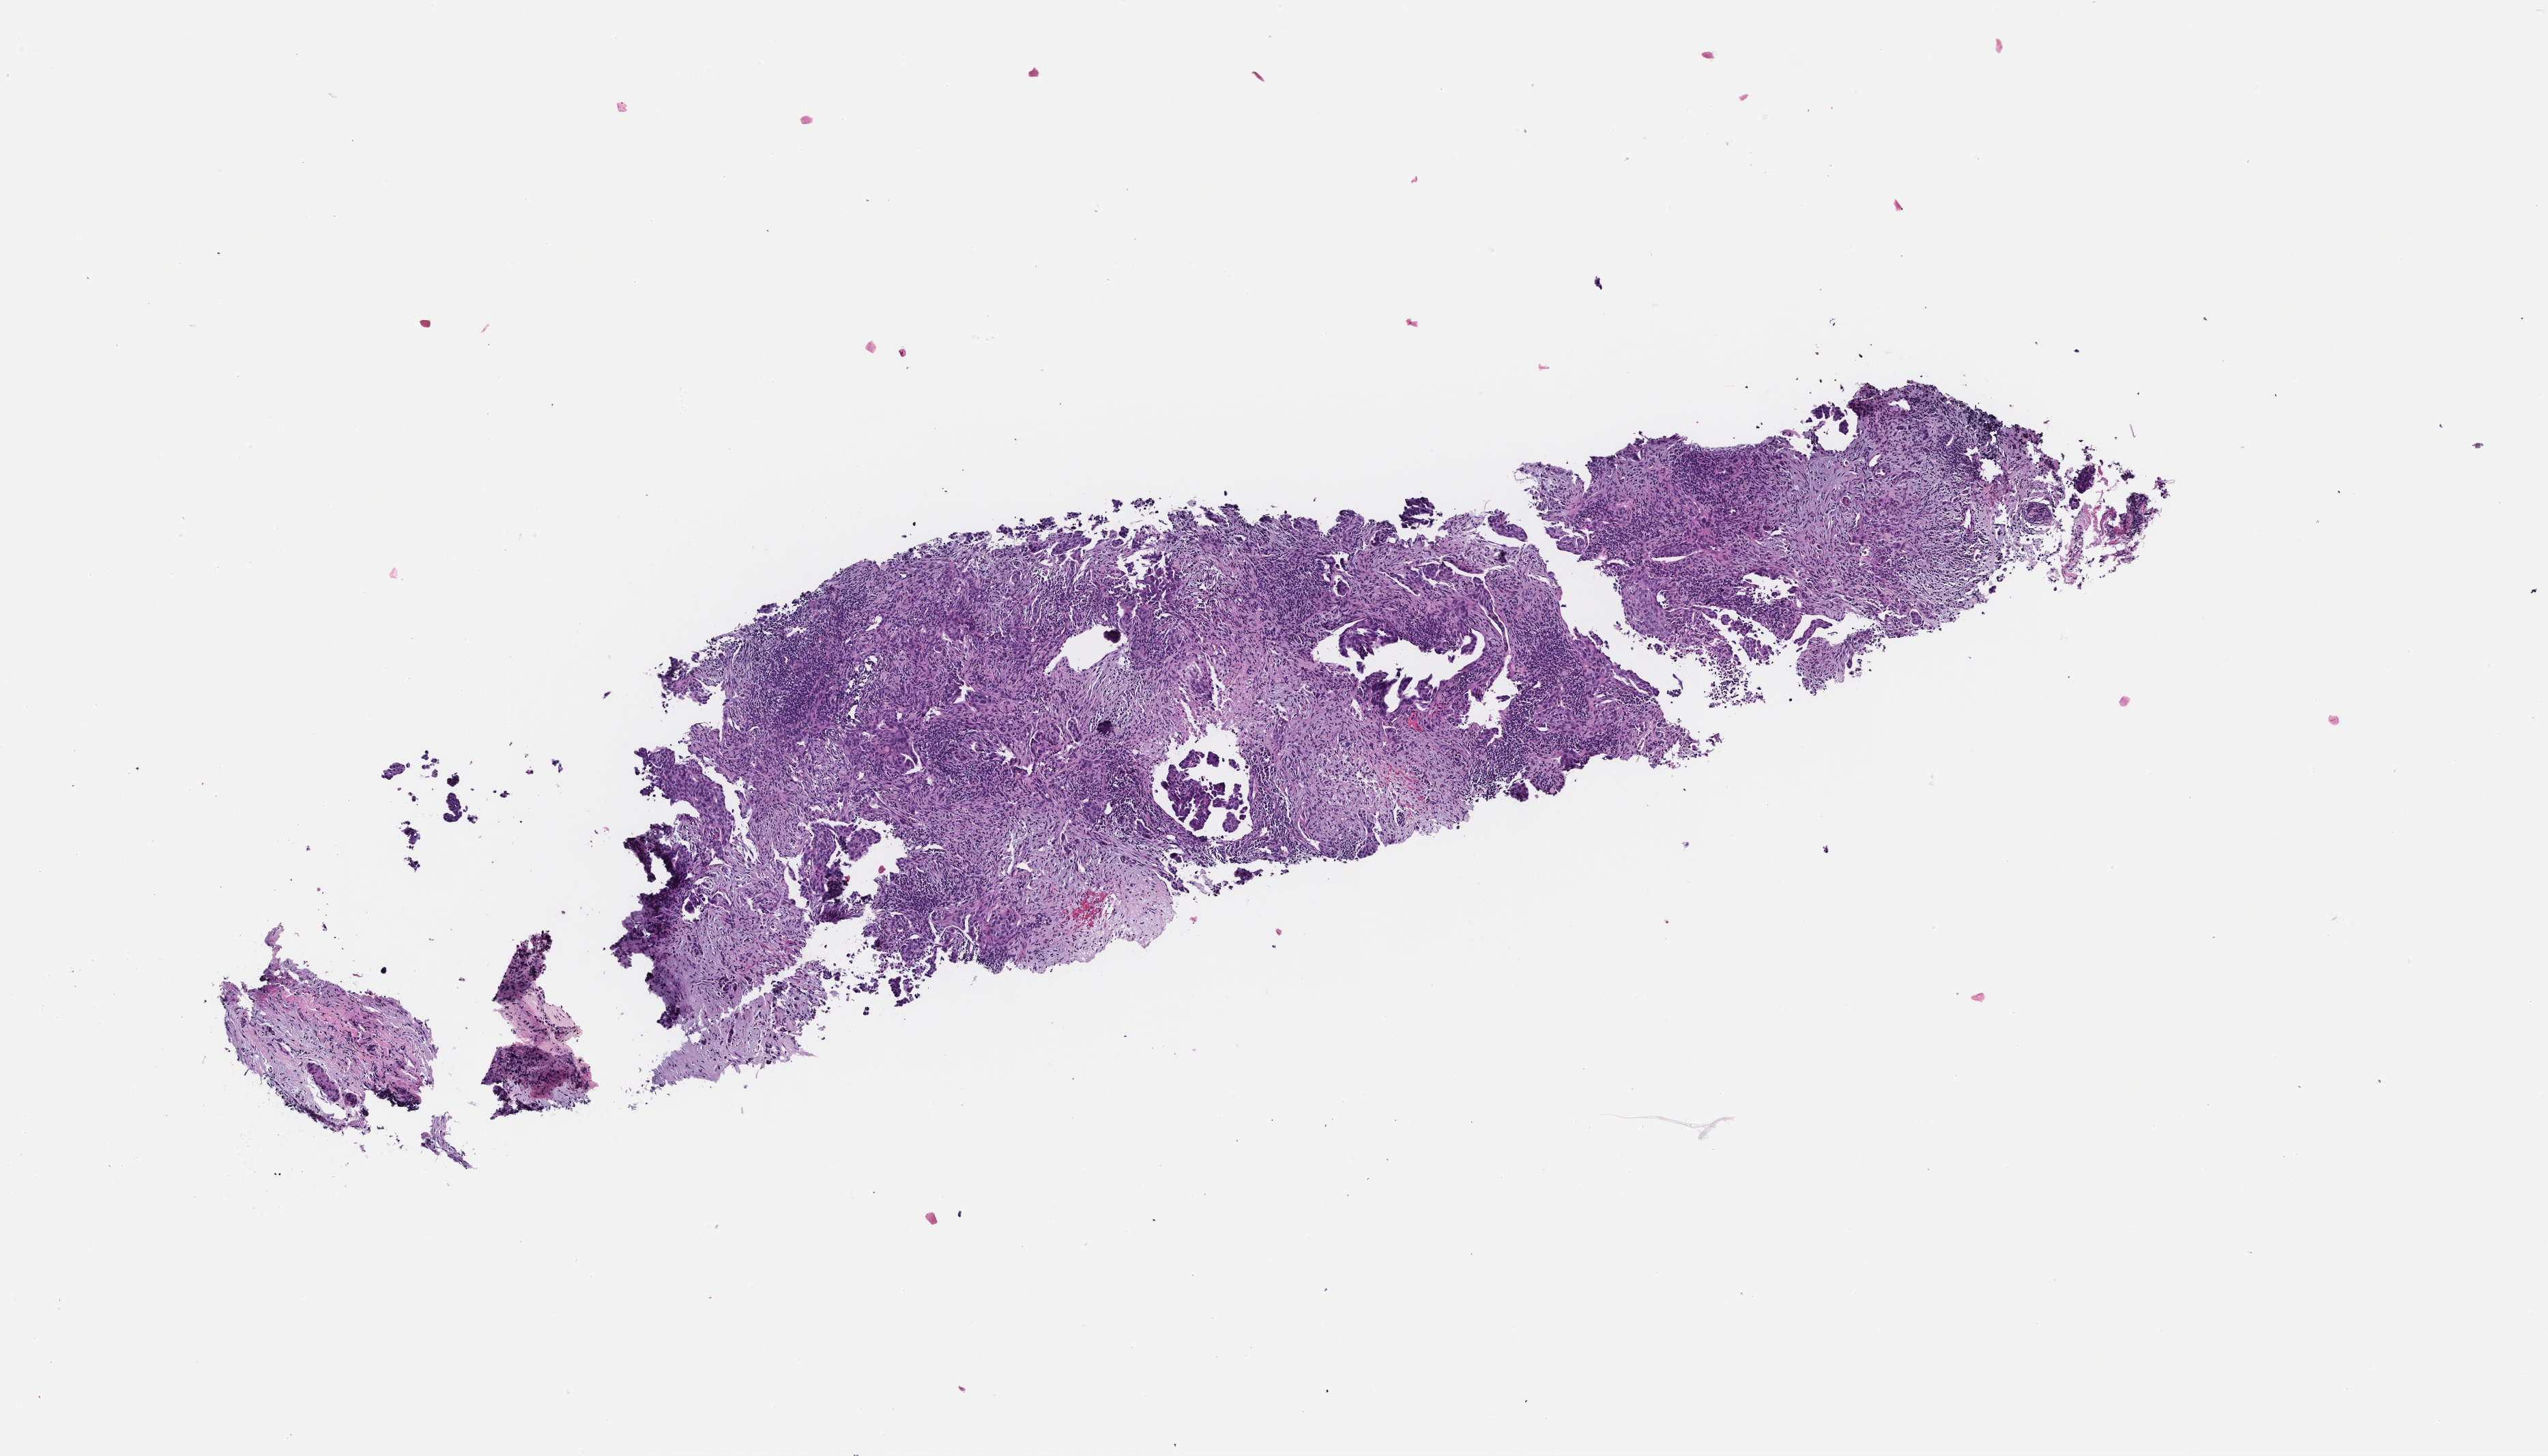
Whole-slide image, haematoxylin and eosin stain, low-resolution overview of the scanned area, about 7.5 x 4.3 mm; formalin-fixed paraffin-embedded section; archival tissue. Patient: male.
This section: metastasis (sampled organ not recorded). Primary diagnosis of the patient: Non-Small Cell Lung Carcinoma.